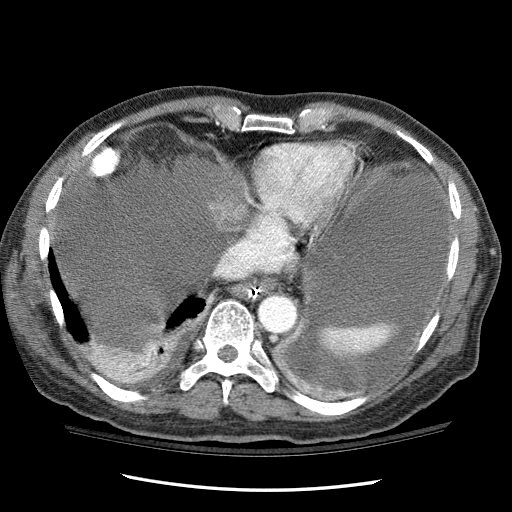
Contrast-enhanced abdominal CT (liver protocol), one axial slice. Slice 98 of 114 in the series (ordered by position). Reconstruction kernel STANDARD. 120 kVp. One of 3 acquisitions stored at this slice position. Soft-tissue window (W 400 / L 40 HU). 2.5 mm slice thickness. 512 × 512 image matrix, field of view 360 × 360 mm. From the clinical record (not read from this slice): diagnosis: hepatocellular carcinoma (patient treated with transarterial chemoembolisation; whether this scan precedes or follows treatment is not stated here); TNM stage (as recorded): Stage-I; Child-Pugh class: C.
Outlined on this slice (semi-automatic segmentation, software-assisted and operator-edited):
- liver parenchyma outside the tumour (the mass and vessels are separate outlines, so this box may not span the whole liver): bounding box <96,346,143,382> (left, top, right, bottom; pixels)
- mass: <210,195,246,232>
- liver vessels: <116,364,133,380>